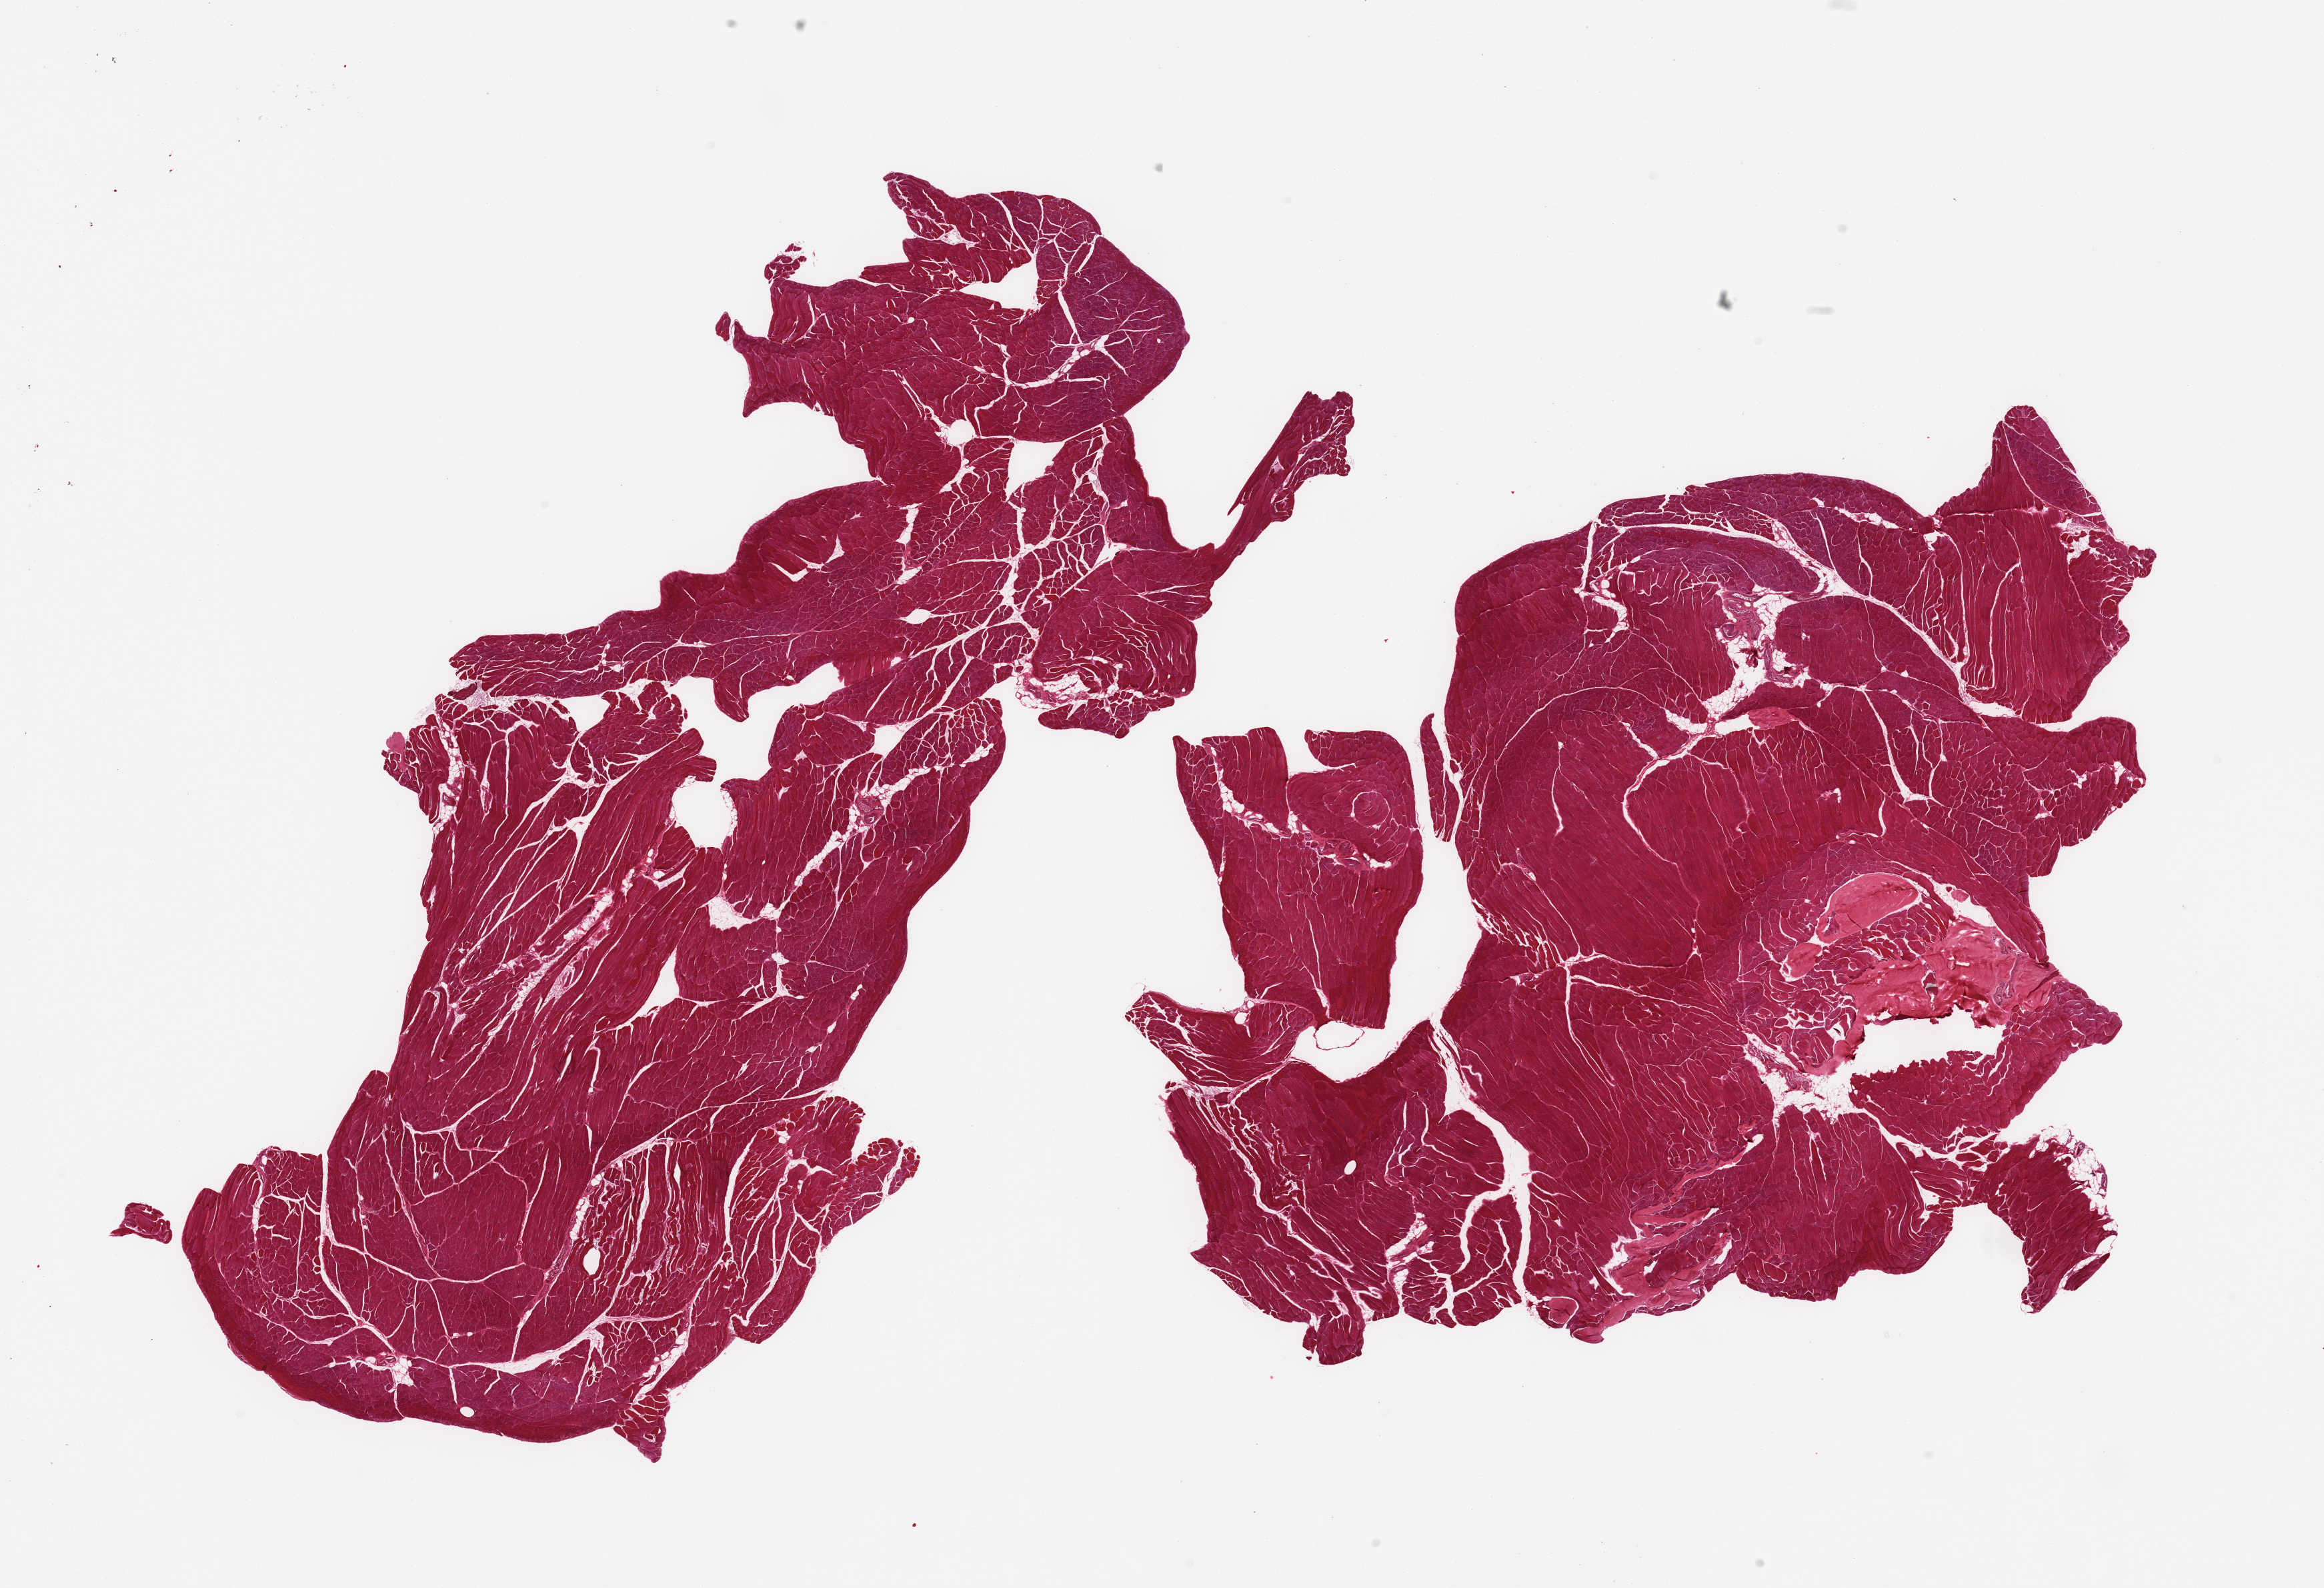
Hematoxylin and eosin (H&E) whole-slide image, low-resolution overview of the scanned area, about 27.6 x 18.8 mm (from a 20x scan). PAXgene-fixed paraffin-embedded (PFPE) section. Sampled site (target tissue): skeletal muscle. Donor tissue sample.
- review note (as recorded): 2 pieces, ~5 - 10% tendon (insertiion site)